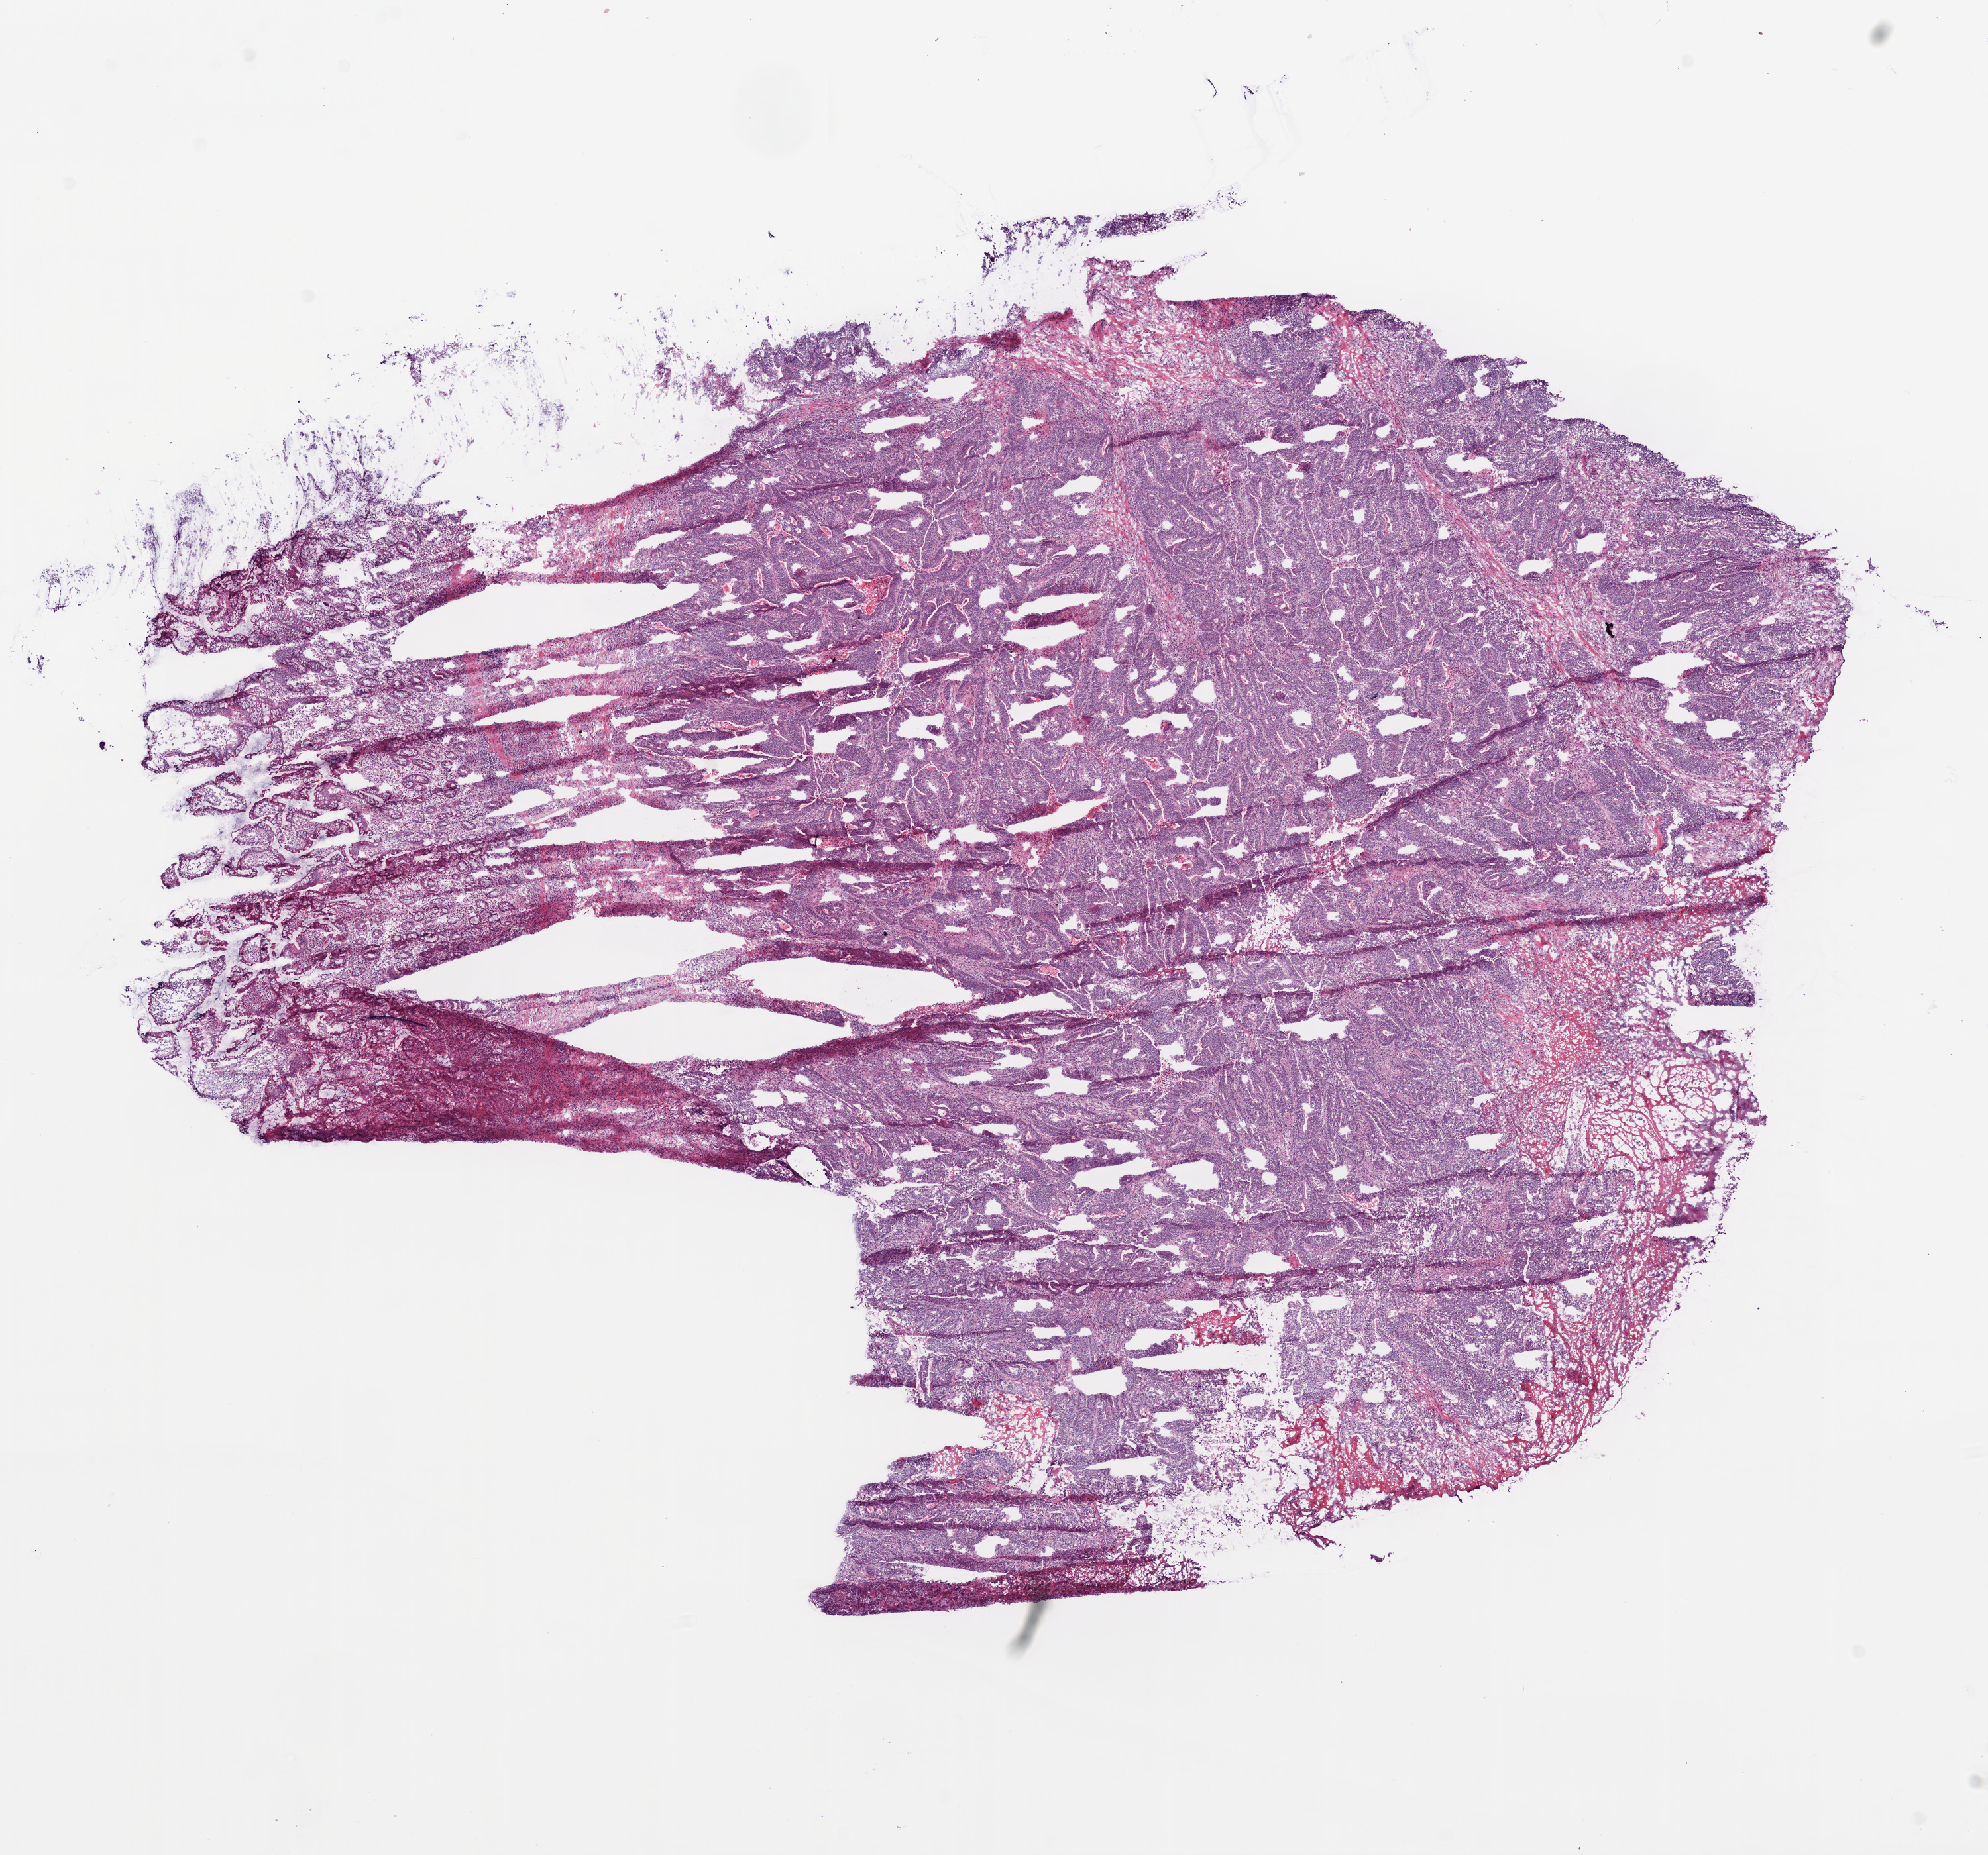
Digitized H&E-stained tissue section (whole slide) — shown as a low-resolution overview of the whole scanned area (about 12.0 x 11.2 mm); frozen section; colon, primary tumour sample. Patient: female, age at initial diagnosis 65 years. Slide review estimates, as recorded: tumour cells 72%, tumour nuclei 75%.
Pathologic diagnosis: Adenocarcinoma, NOS (cecum).